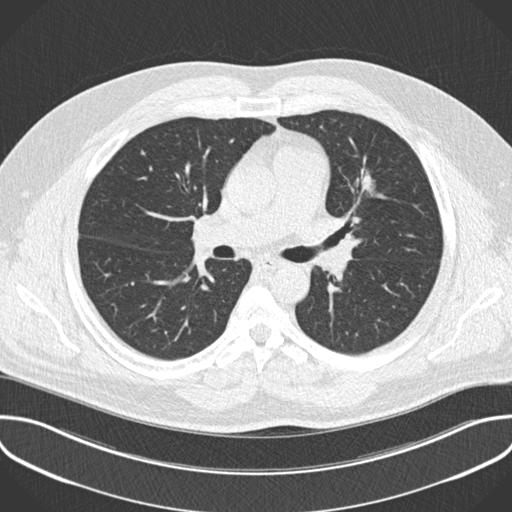
Chest CT (low-dose screening protocol), one axial image; baseline annual screen; lung window (W 1500 / L -600 HU); 2 mm slice thickness; 120 kVp; 512 × 512 image matrix, field of view 386 × 386 mm. Male participant, aged 55 years at enrolment. Former smoker at enrolment.
Expert reader's lesion annotation, bounding box [x1, y1, x2, y2] px = [346, 159, 391, 194]. The exam's reader record, not a measurement of the box and not confirmed to be the same lesion: non-calcified nodule or mass ≥4 mm, lingula, 13 × 12 mm, spiculated (stellate) margins, soft tissue attenuation.